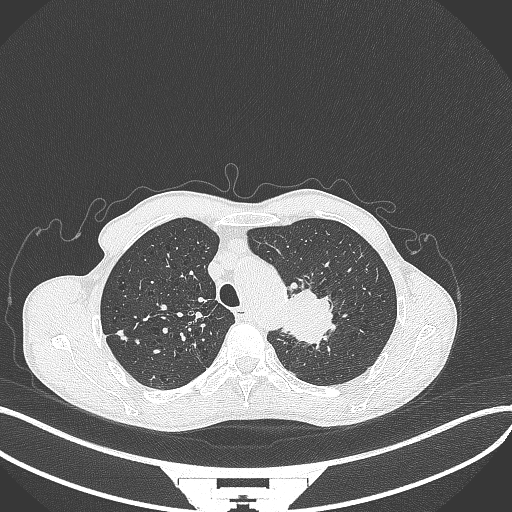
Chest CT, one axial slice; position 327 of 386 along the scan axis; reconstruction kernel B70f; lung window (W 1500 / L -600 HU); 1 mm slice thickness; 512 × 512 image matrix, field of view 400 × 400 mm. Male patient, age 65 years. Case-level facts recorded for this patient, not image findings: clinical TNM (as recorded): T2b N0 M0.
Outlined on this slice (bounding box drawn by a radiologist):
- lung tumour (recorded histology: adenocarcinoma): bounding box <276,283,338,353> (left, top, right, bottom; pixels)